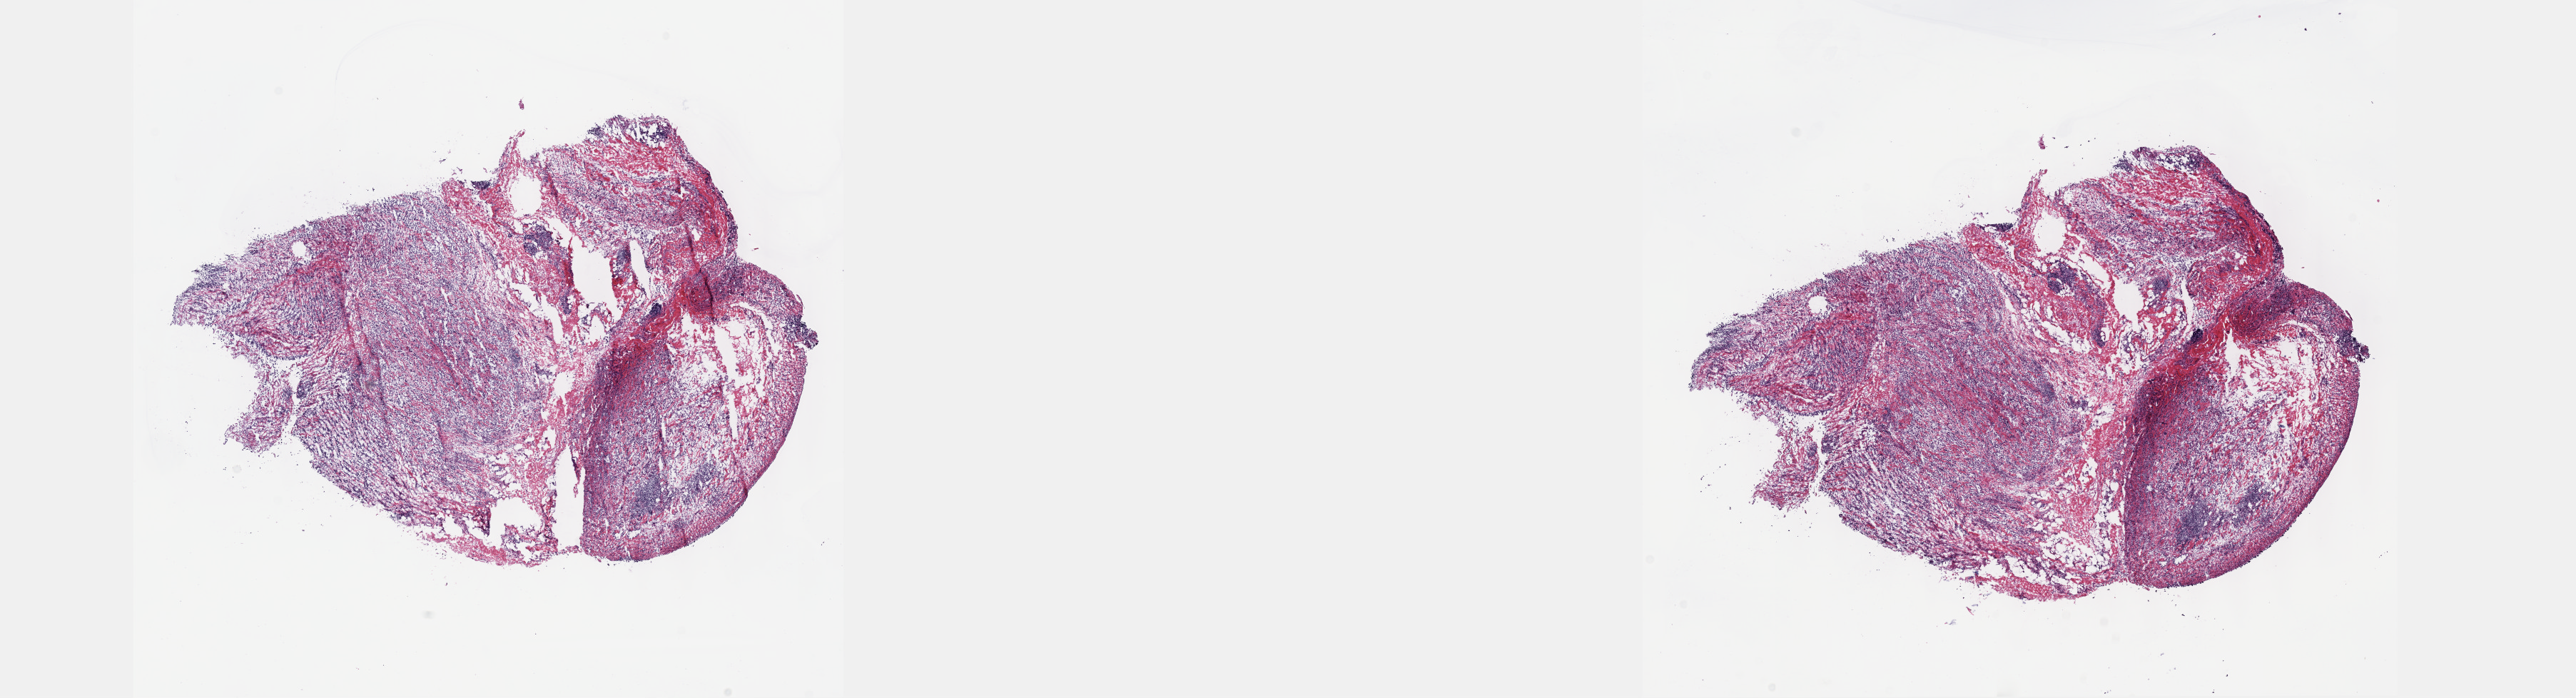
H&E-stained whole-slide image, a low-resolution overview of the entire scanned area, about 29.2 x 7.9 mm; frozen section from the top of the tissue portion; sample: primary tumour, mesothelium. Male patient; age at initial diagnosis 62 years. Composition of this section per pathologist review: tumour cells 70%, tumour nuclei 70%, normal cells 0%, stromal cells 30%, necrosis 0%. Infiltration values recorded for this section: lymphocyte infiltration 5%, monocyte infiltration 1%, neutrophil infiltration 5%.
AJCC pathologic stage: III. Diagnosis: Epithelioid mesothelioma, malignant (pleura, NOS).